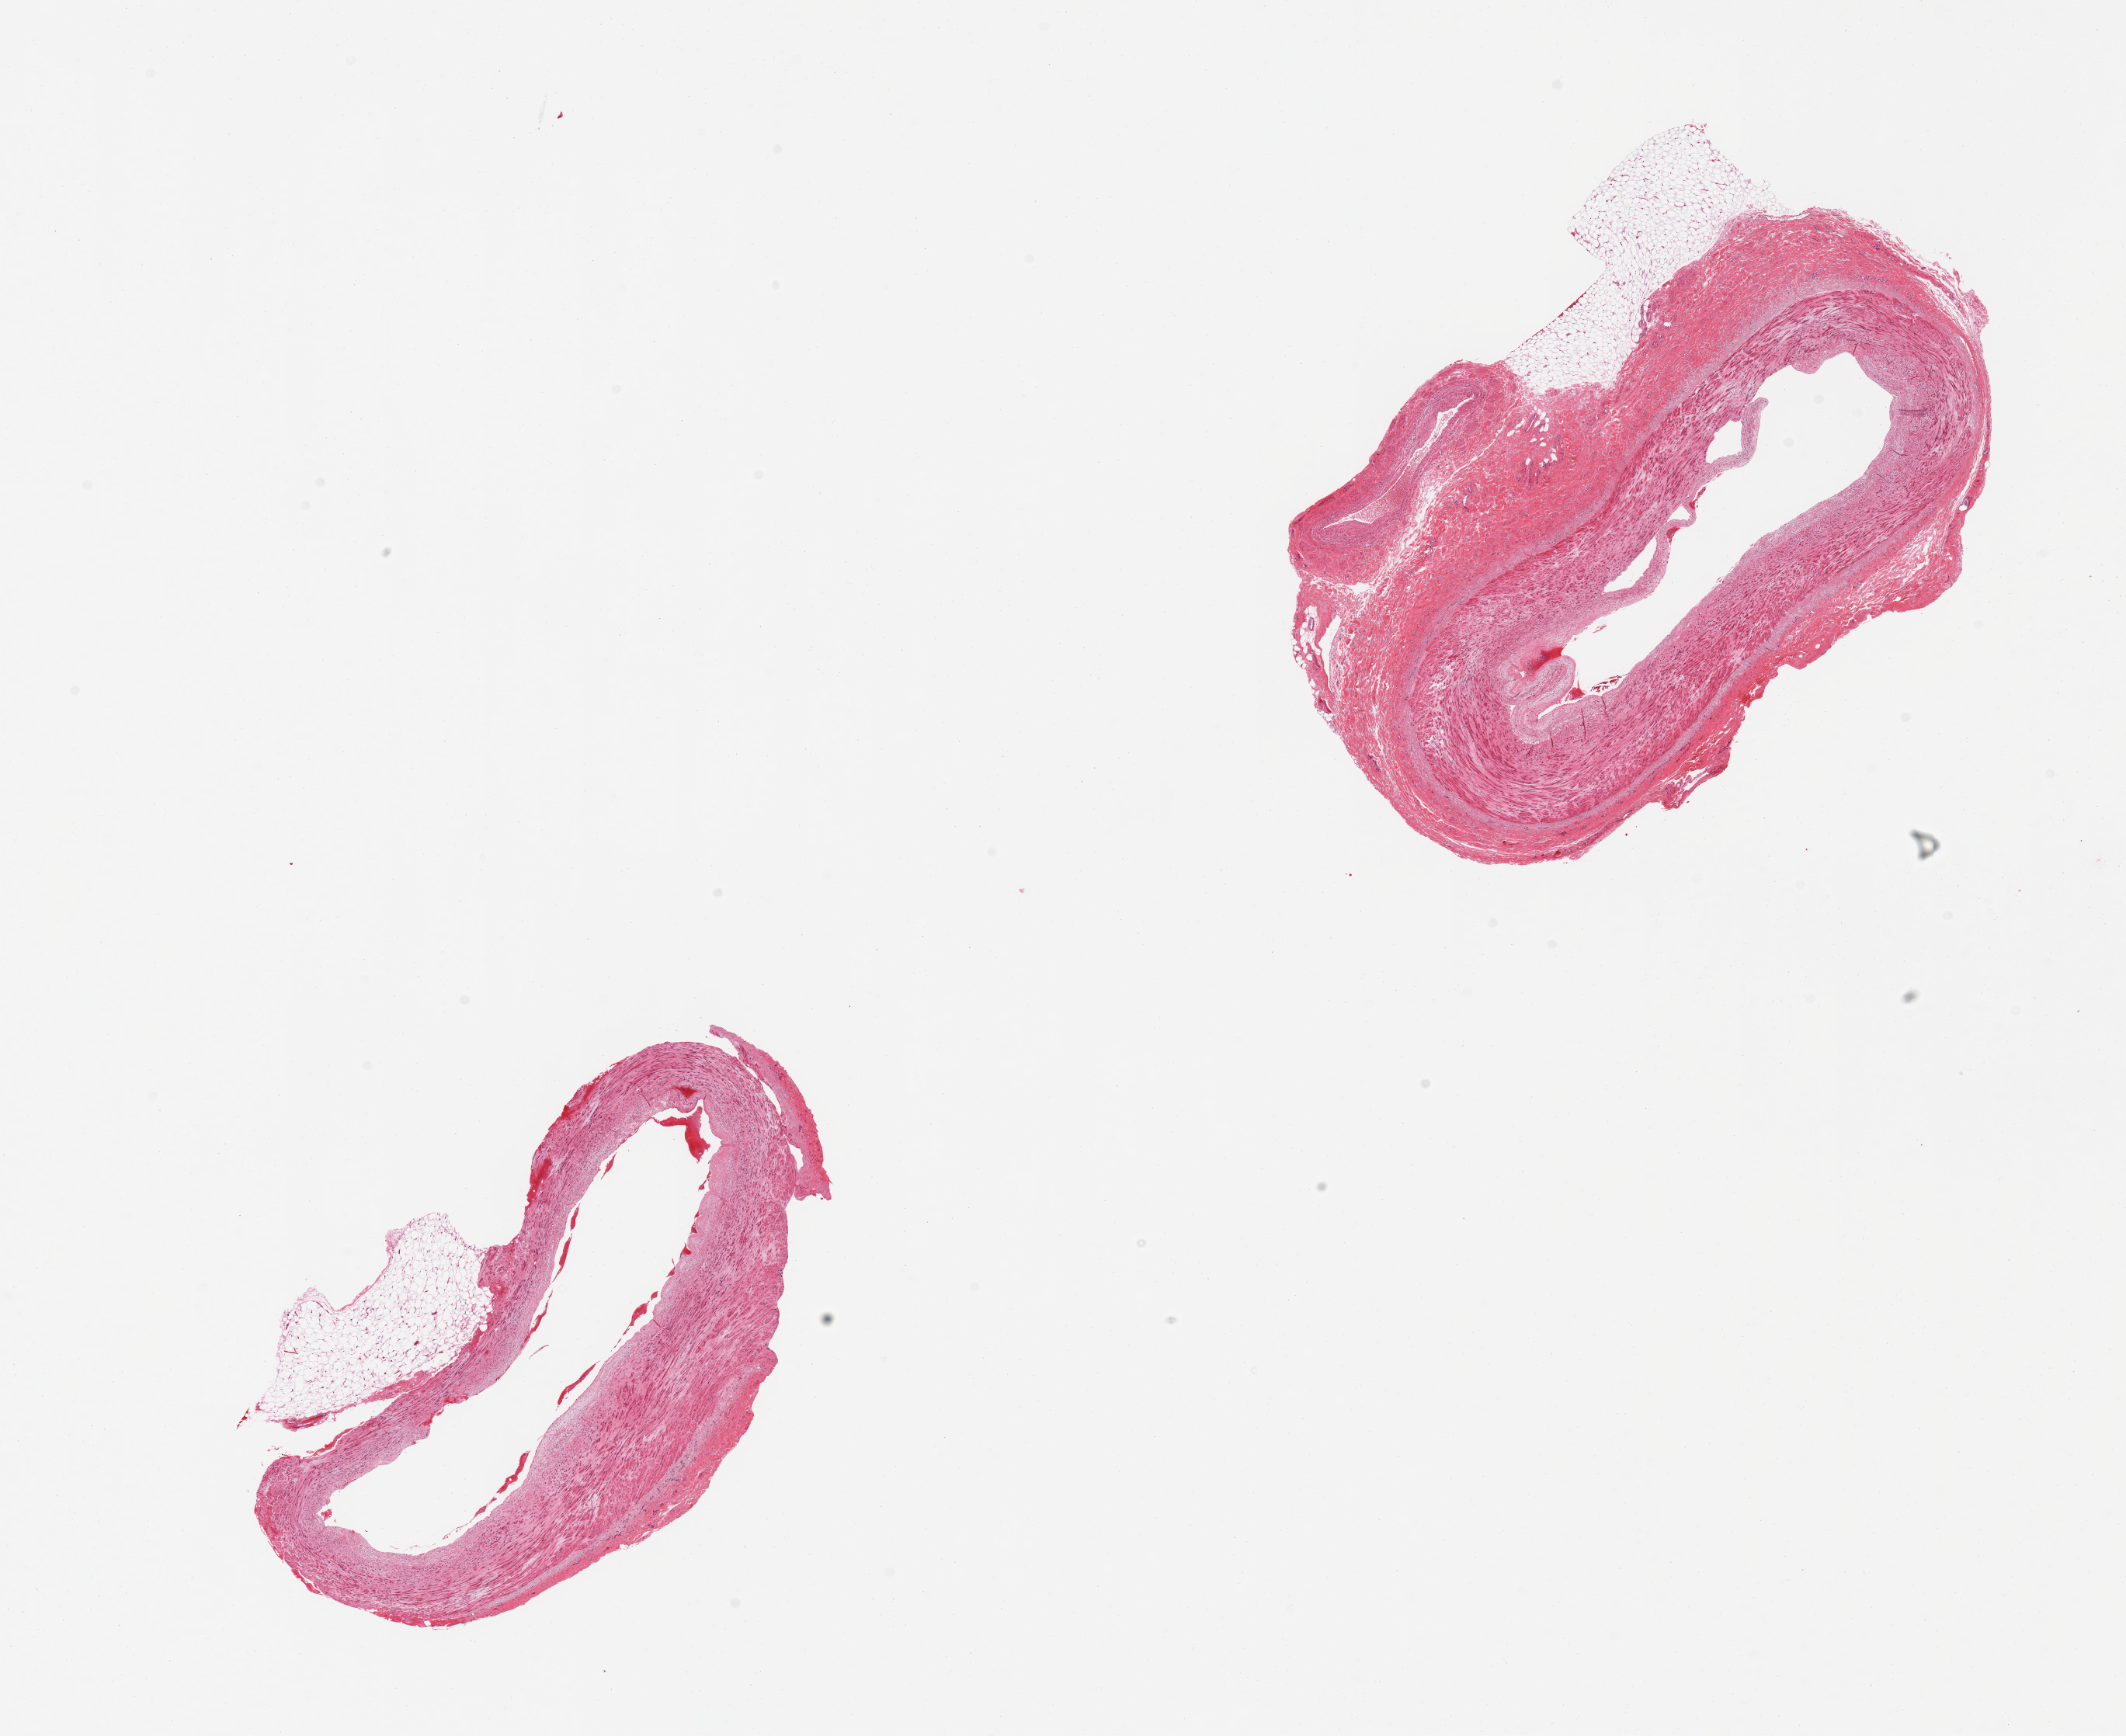
Whole-slide image, H&E stain, a low-resolution overview of the entire scanned area, about 21.7 x 17.7 mm; PAXgene-fixed paraffin-embedded (PFPE) section; section of tibial artery (target tissue); tissue donor sample. Male donor.
Reviewer comment on this tissue sample: 2 pieces, small attachment of fat on both (~10%).